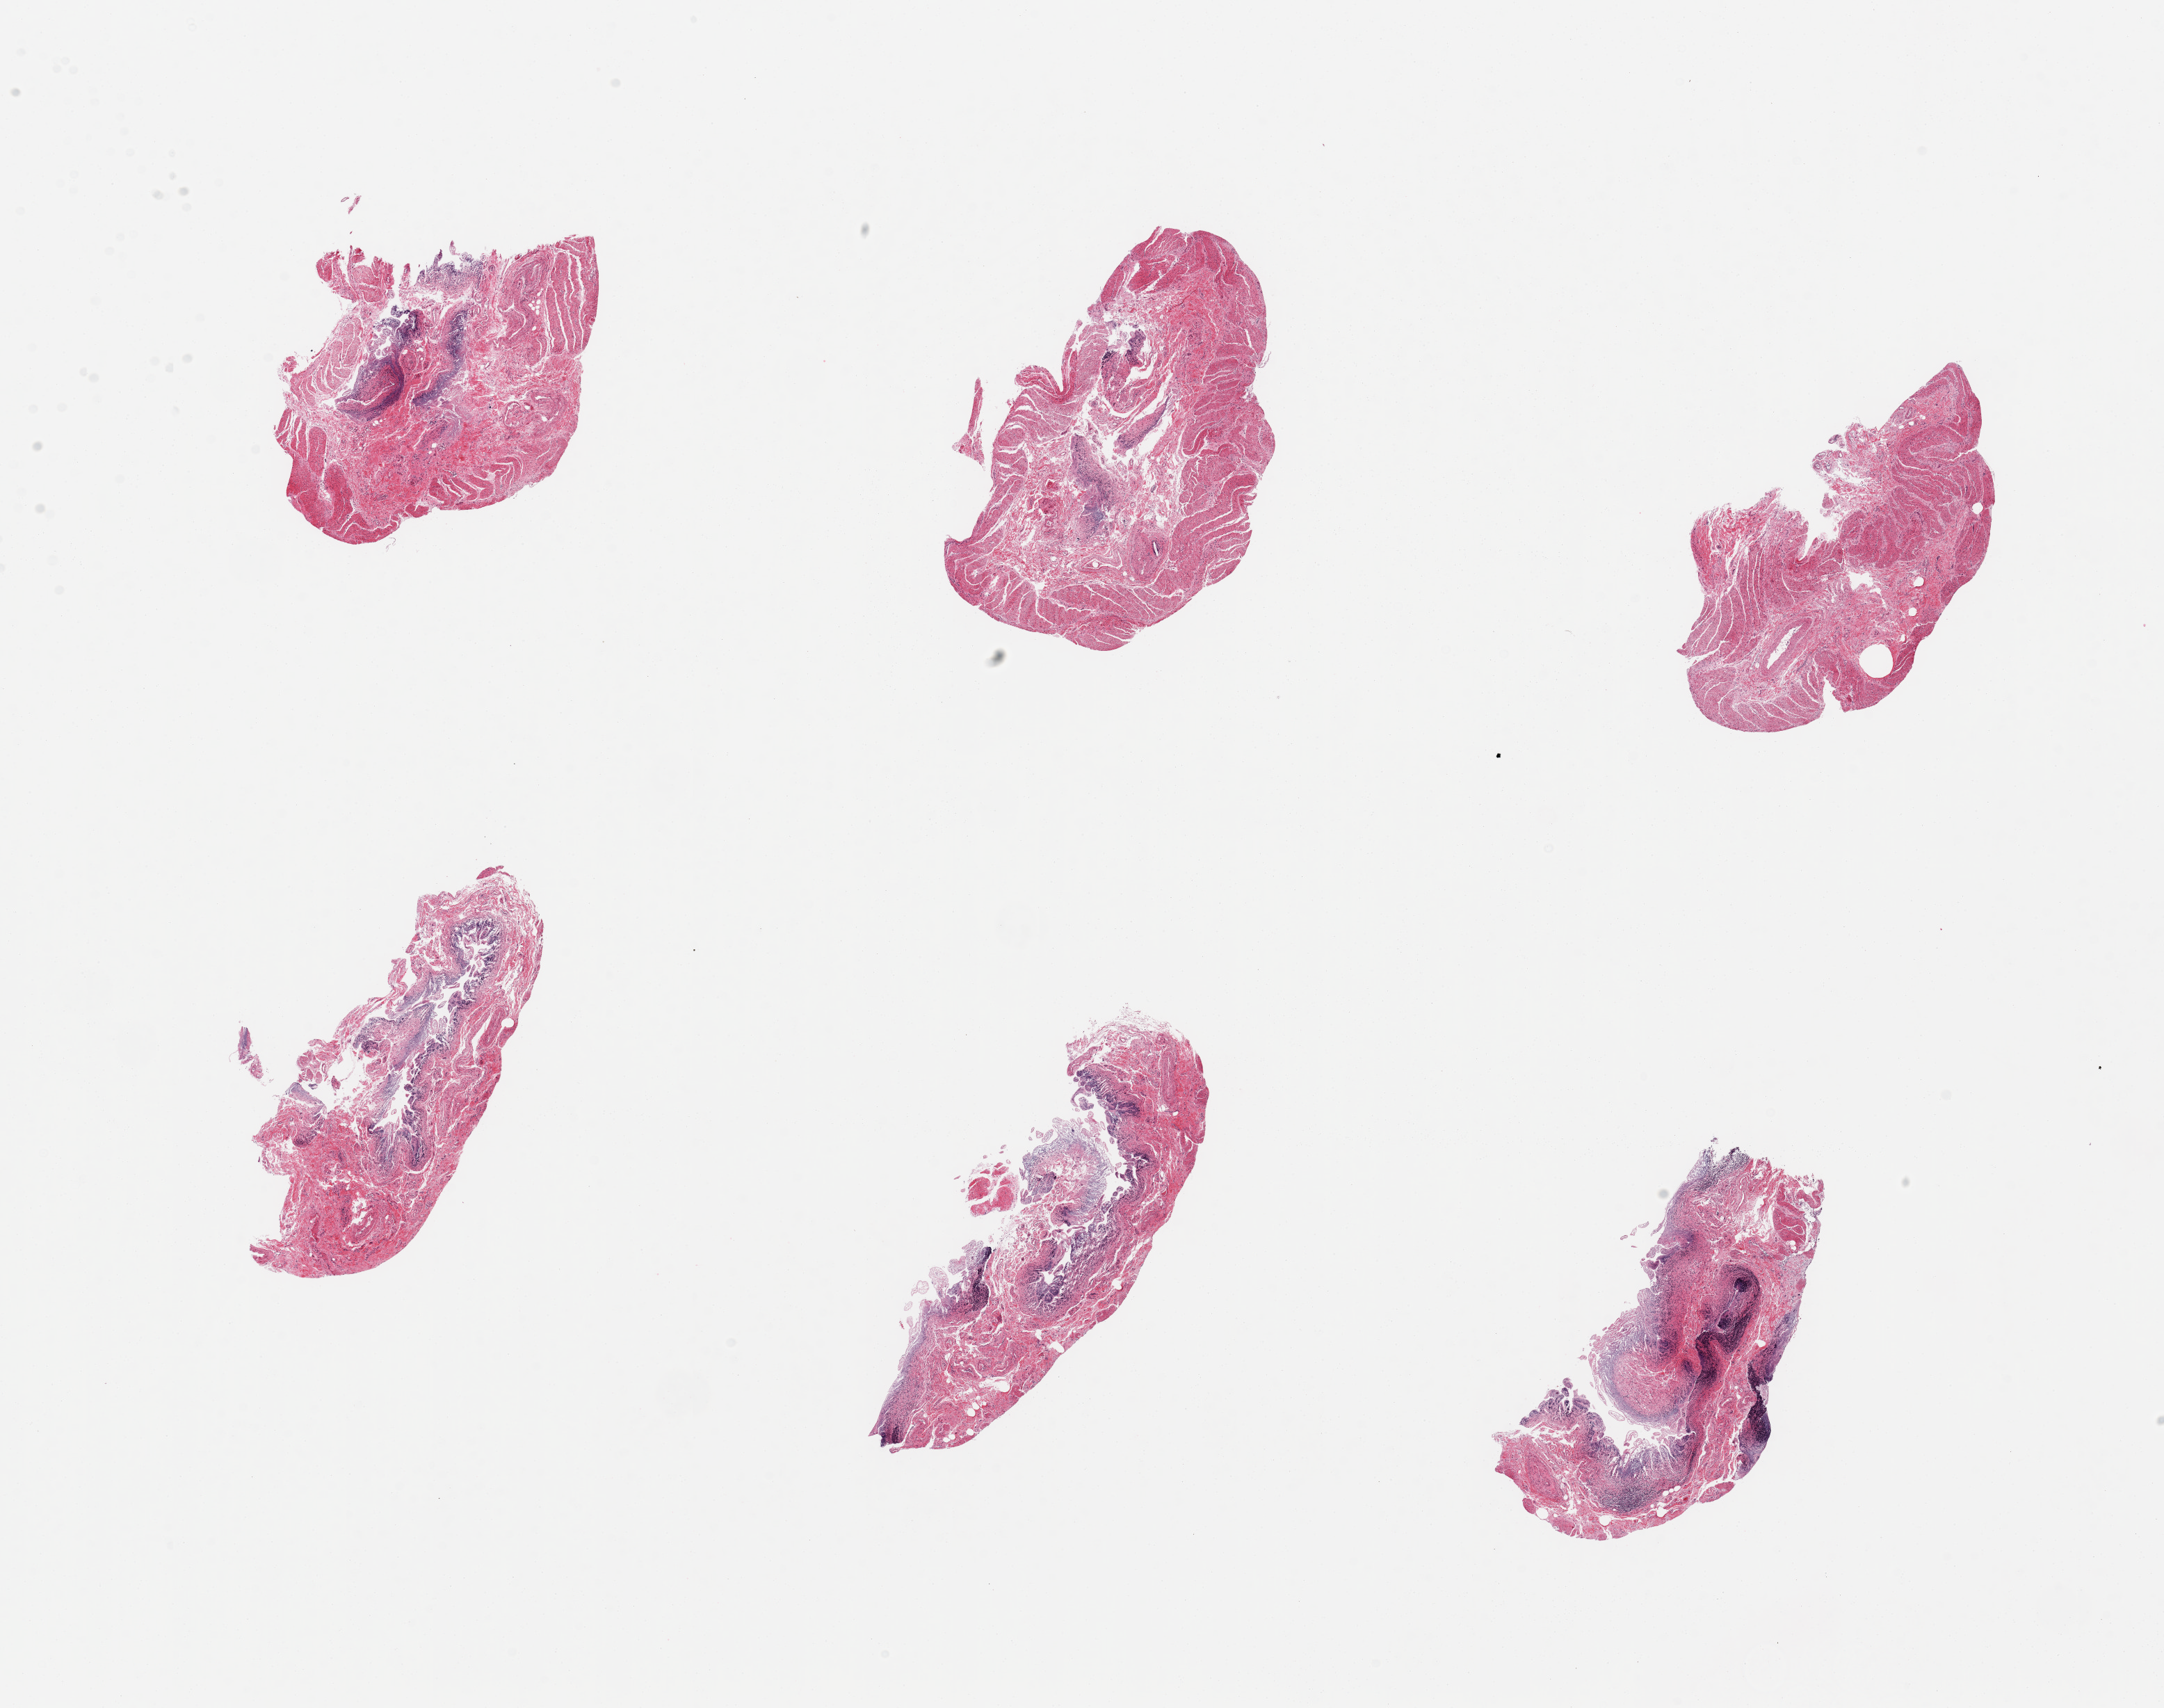
Whole-slide image, hematoxylin and eosin (H&E) stain, a low-resolution overview of the entire scanned area, about 24.6 x 19.4 mm (from a 20x scan), PAXgene-fixed paraffin-embedded (PFPE) section, target tissue: ileum, donor tissue sample. Male donor.
Review note (as recorded): 6 pieces, ~10% lymphoid aggregates.